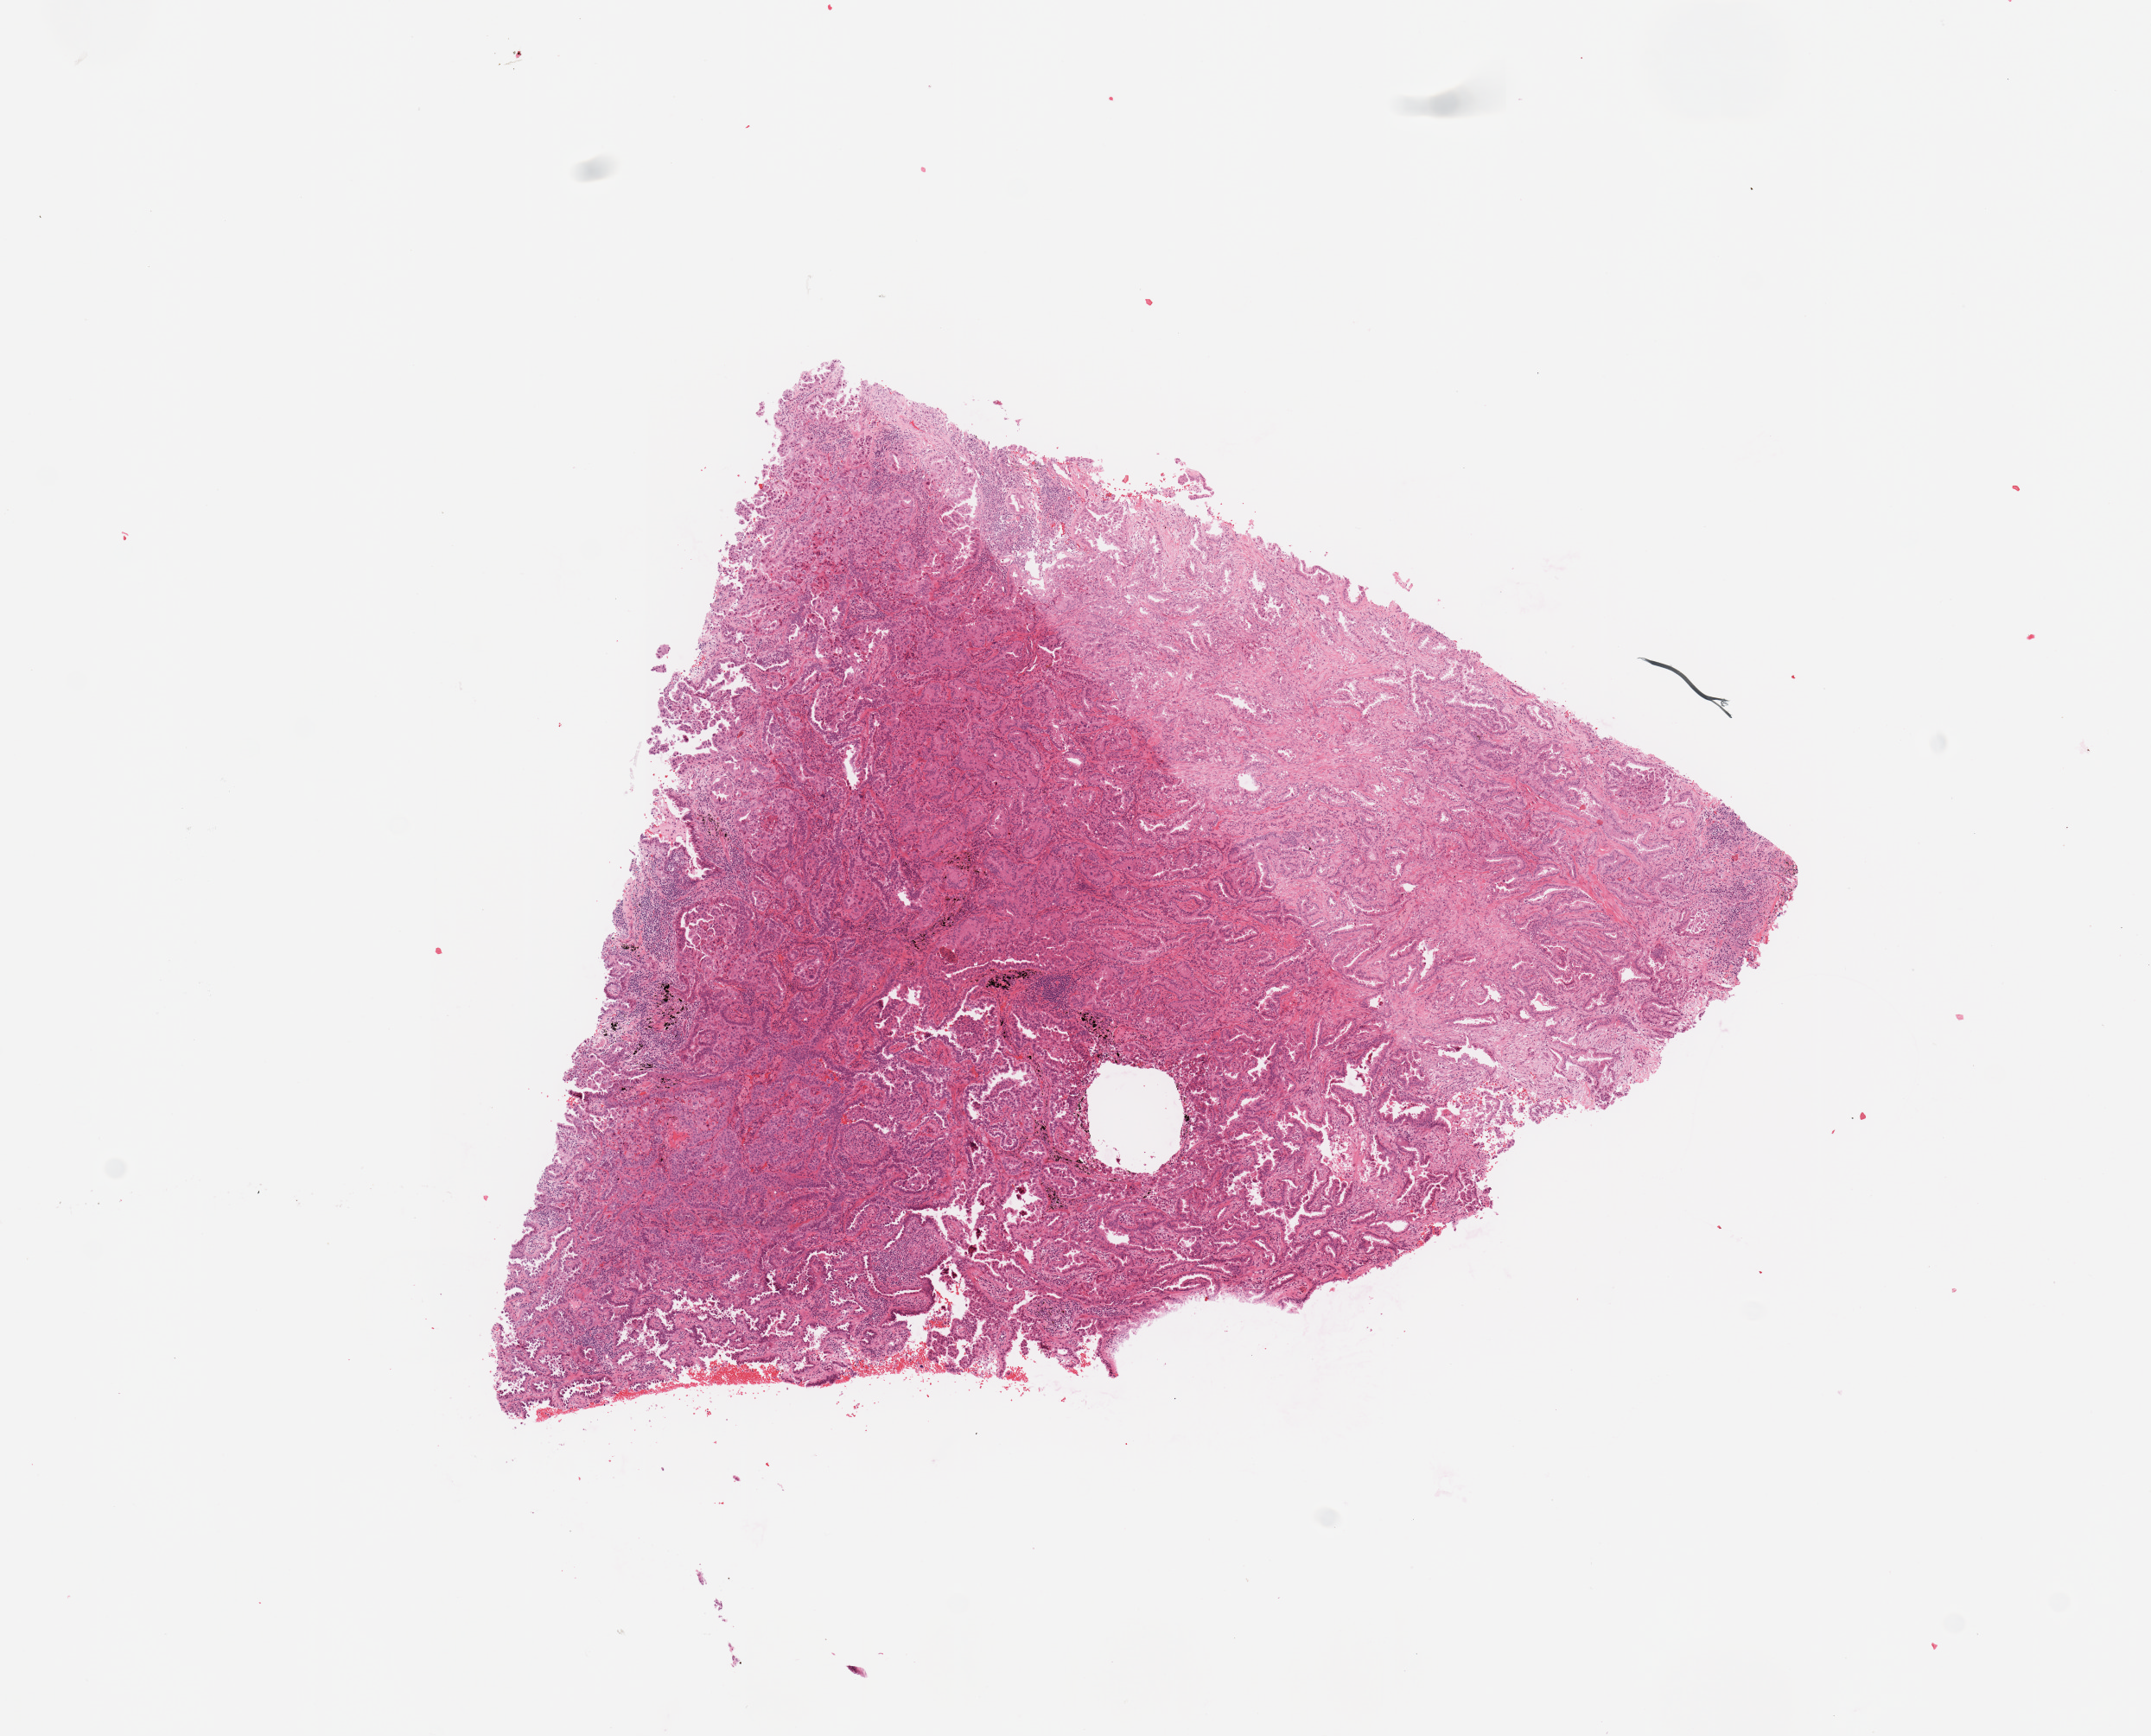
H&E whole-slide image, whole scanned area (about 9.8 x 7.9 mm, acquisition: 20x scan) shown as a low-resolution overview; lung, tumour tissue. Male, 51 y/o. Histologic grade: G2 (moderately differentiated).
* histologic diagnosis: Adenocarcinoma, NOS
* AJCC pathologic stage: IA3
* primary tumour site (as recorded): left lower lobe